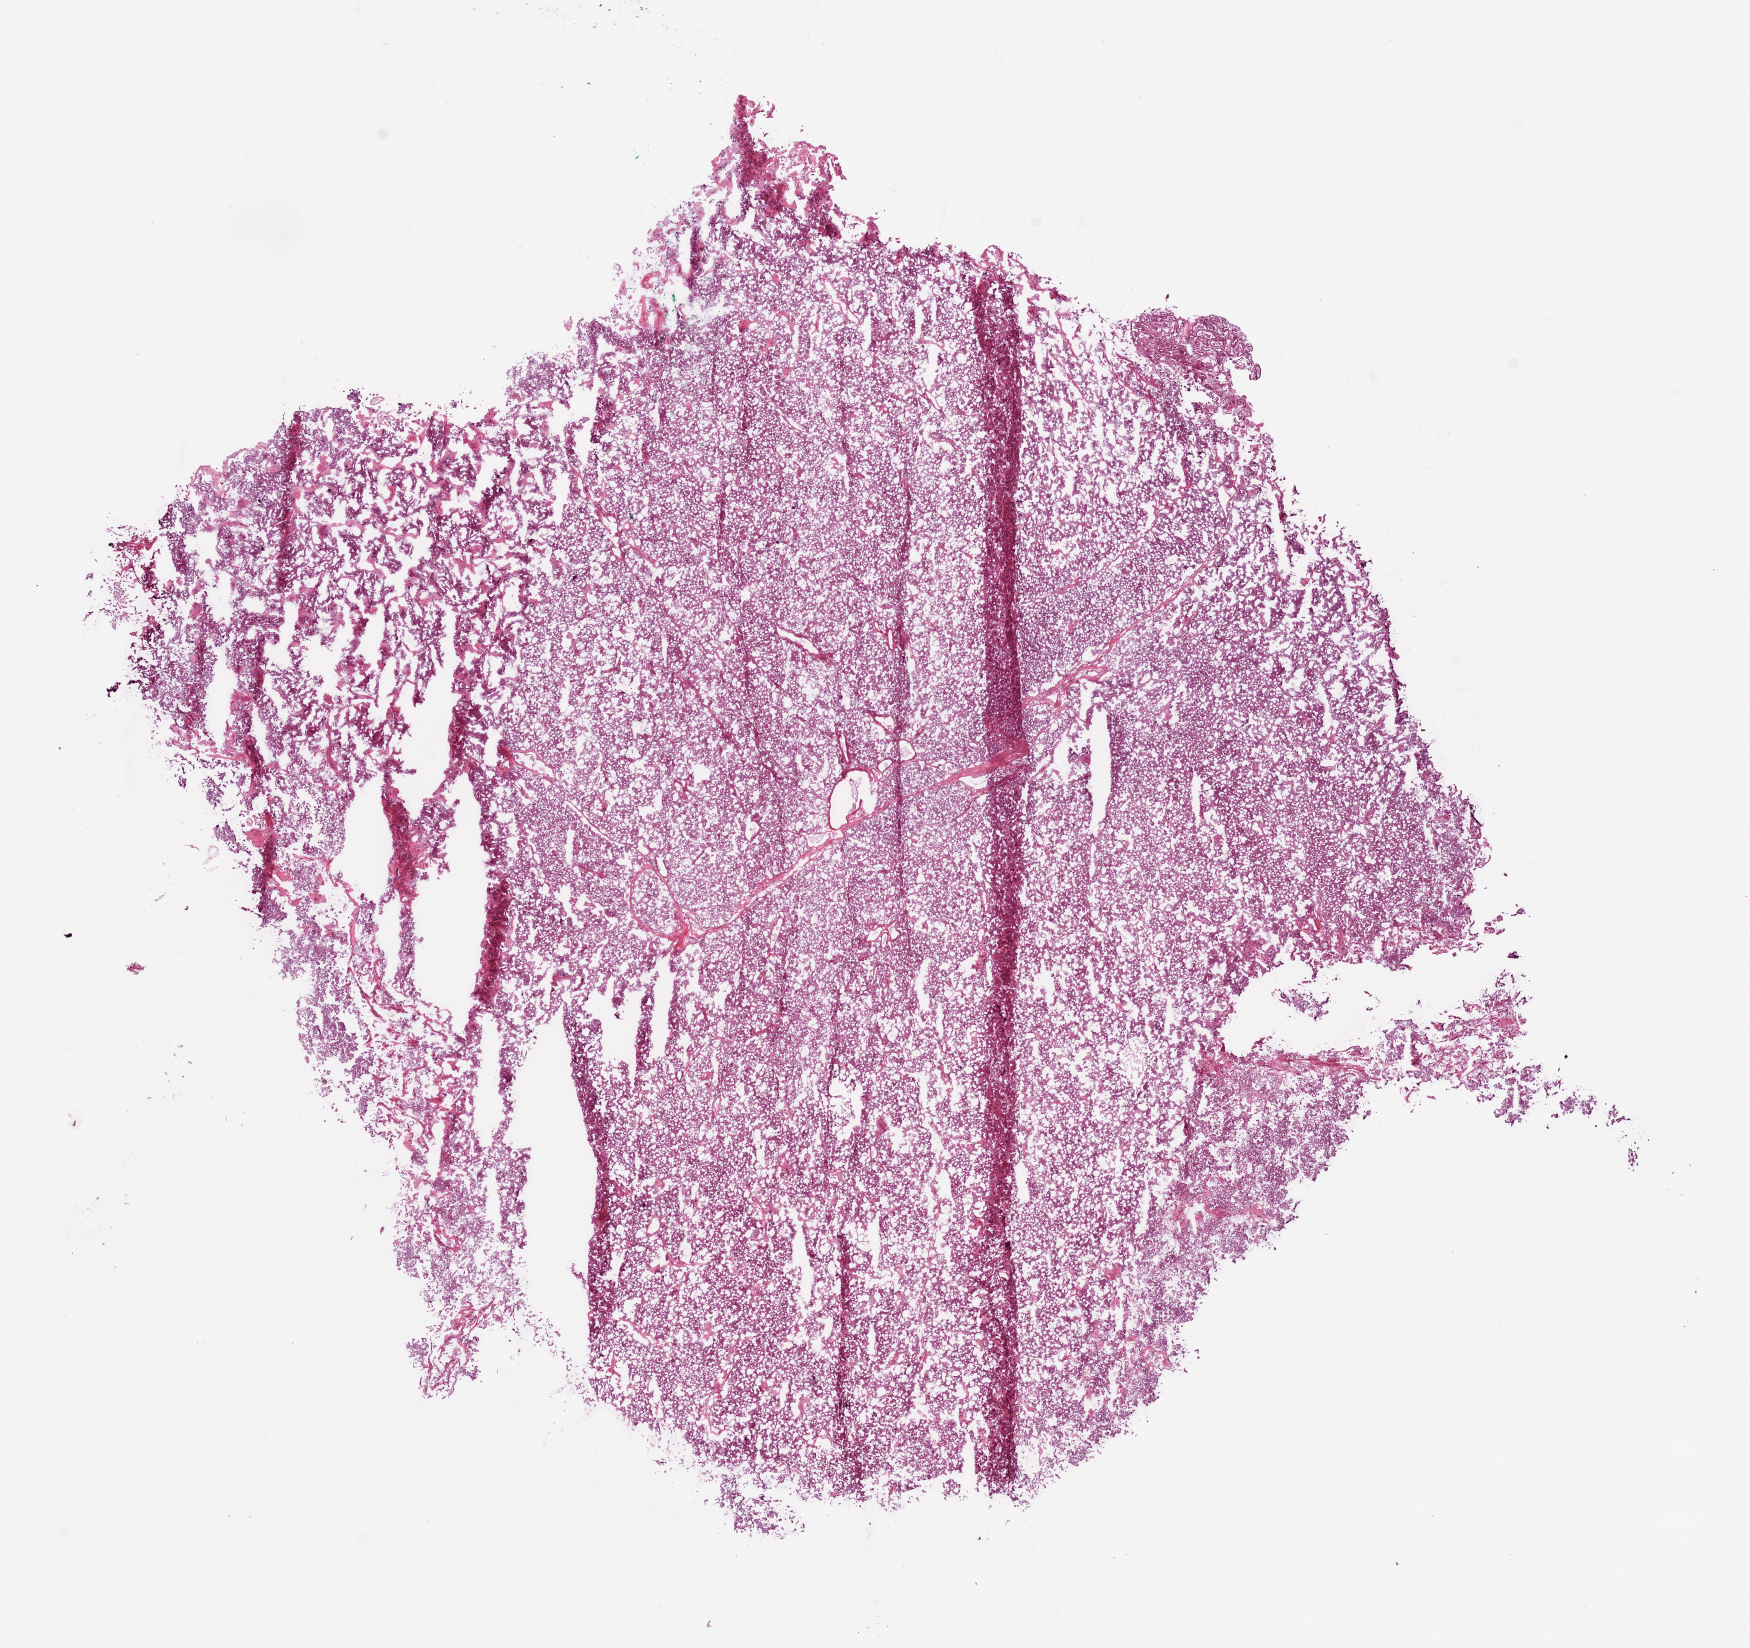
H&E-stained whole-slide image — a low-resolution overview of the entire scanned area, about 14.0 x 13.2 mm; frozen section from the bottom of the tissue portion; primary tumour sample from the kidney. Male patient; age at initial diagnosis 40 years. Composition of this section per pathologist review: tumour cells 90%, tumour nuclei 85%.
Pathologic diagnosis: Clear cell adenocarcinoma, NOS.